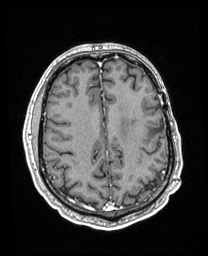
Brain MRI from a brain-tumour surgery series, one axial slice. T1-weighted post-contrast. 208 × 256 image matrix, field of view 211 × 260 mm. Case-level facts recorded for this patient, not image findings: histopathology: Astrocytoma; WHO grade: 3; IDH mutation: yes.
Structures marked on this image (expert manual segmentation):
- previous resection cavity: bounding box [x1, y1, x2, y2] px = [158, 120, 164, 131]